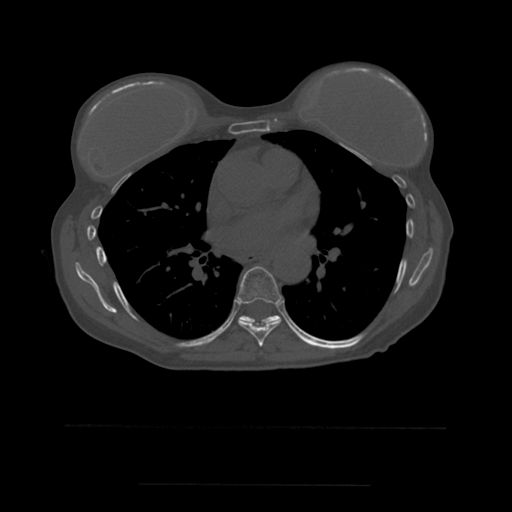
CT including the spine, one axial slice. Slice 352 of 544 in the series (ordered by position). Bone window (W 1800 / L 400 HU). 512 × 512 image matrix, field of view 350 × 350 mm. Patient age 58 years. Case-level facts recorded for this patient, not image findings: primary cancer: lung.
Annotated regions visible in this slice (semi-automatic segmentation, software-assisted and operator-edited):
- T7 vertebra: box from (x=237, y=267) to (x=282, y=347) px
- T8 vertebra: (x=239, y=316)–(x=281, y=327)